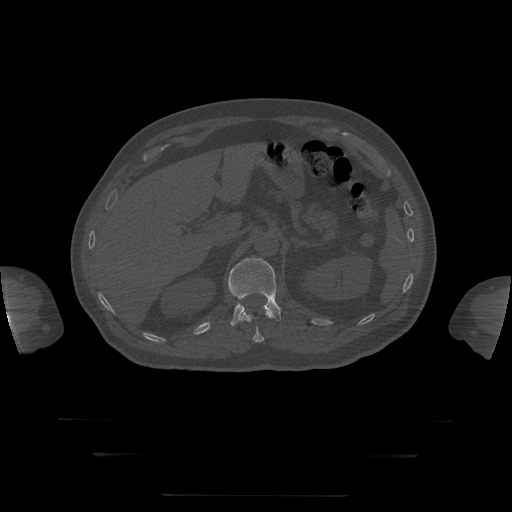
CT including the spine, one axial slice; position 59 of 397 along the scan axis; bone window (W 1800 / L 400 HU); 1.25 mm slice thickness; 512 × 512 image matrix, field of view 510 × 510 mm. Patient age 73 years. Case-level facts recorded for this patient, not image findings: primary cancer: prostate.
Outlined on this slice (semi-automatically segmented with operator editing):
- L1 vertebra: bounding box (x1, y1, x2, y2) in pixels: (228, 258, 282, 326)
- T12 vertebra: (240, 312, 271, 343)
- T8 vertebra: (243, 307, 271, 314)